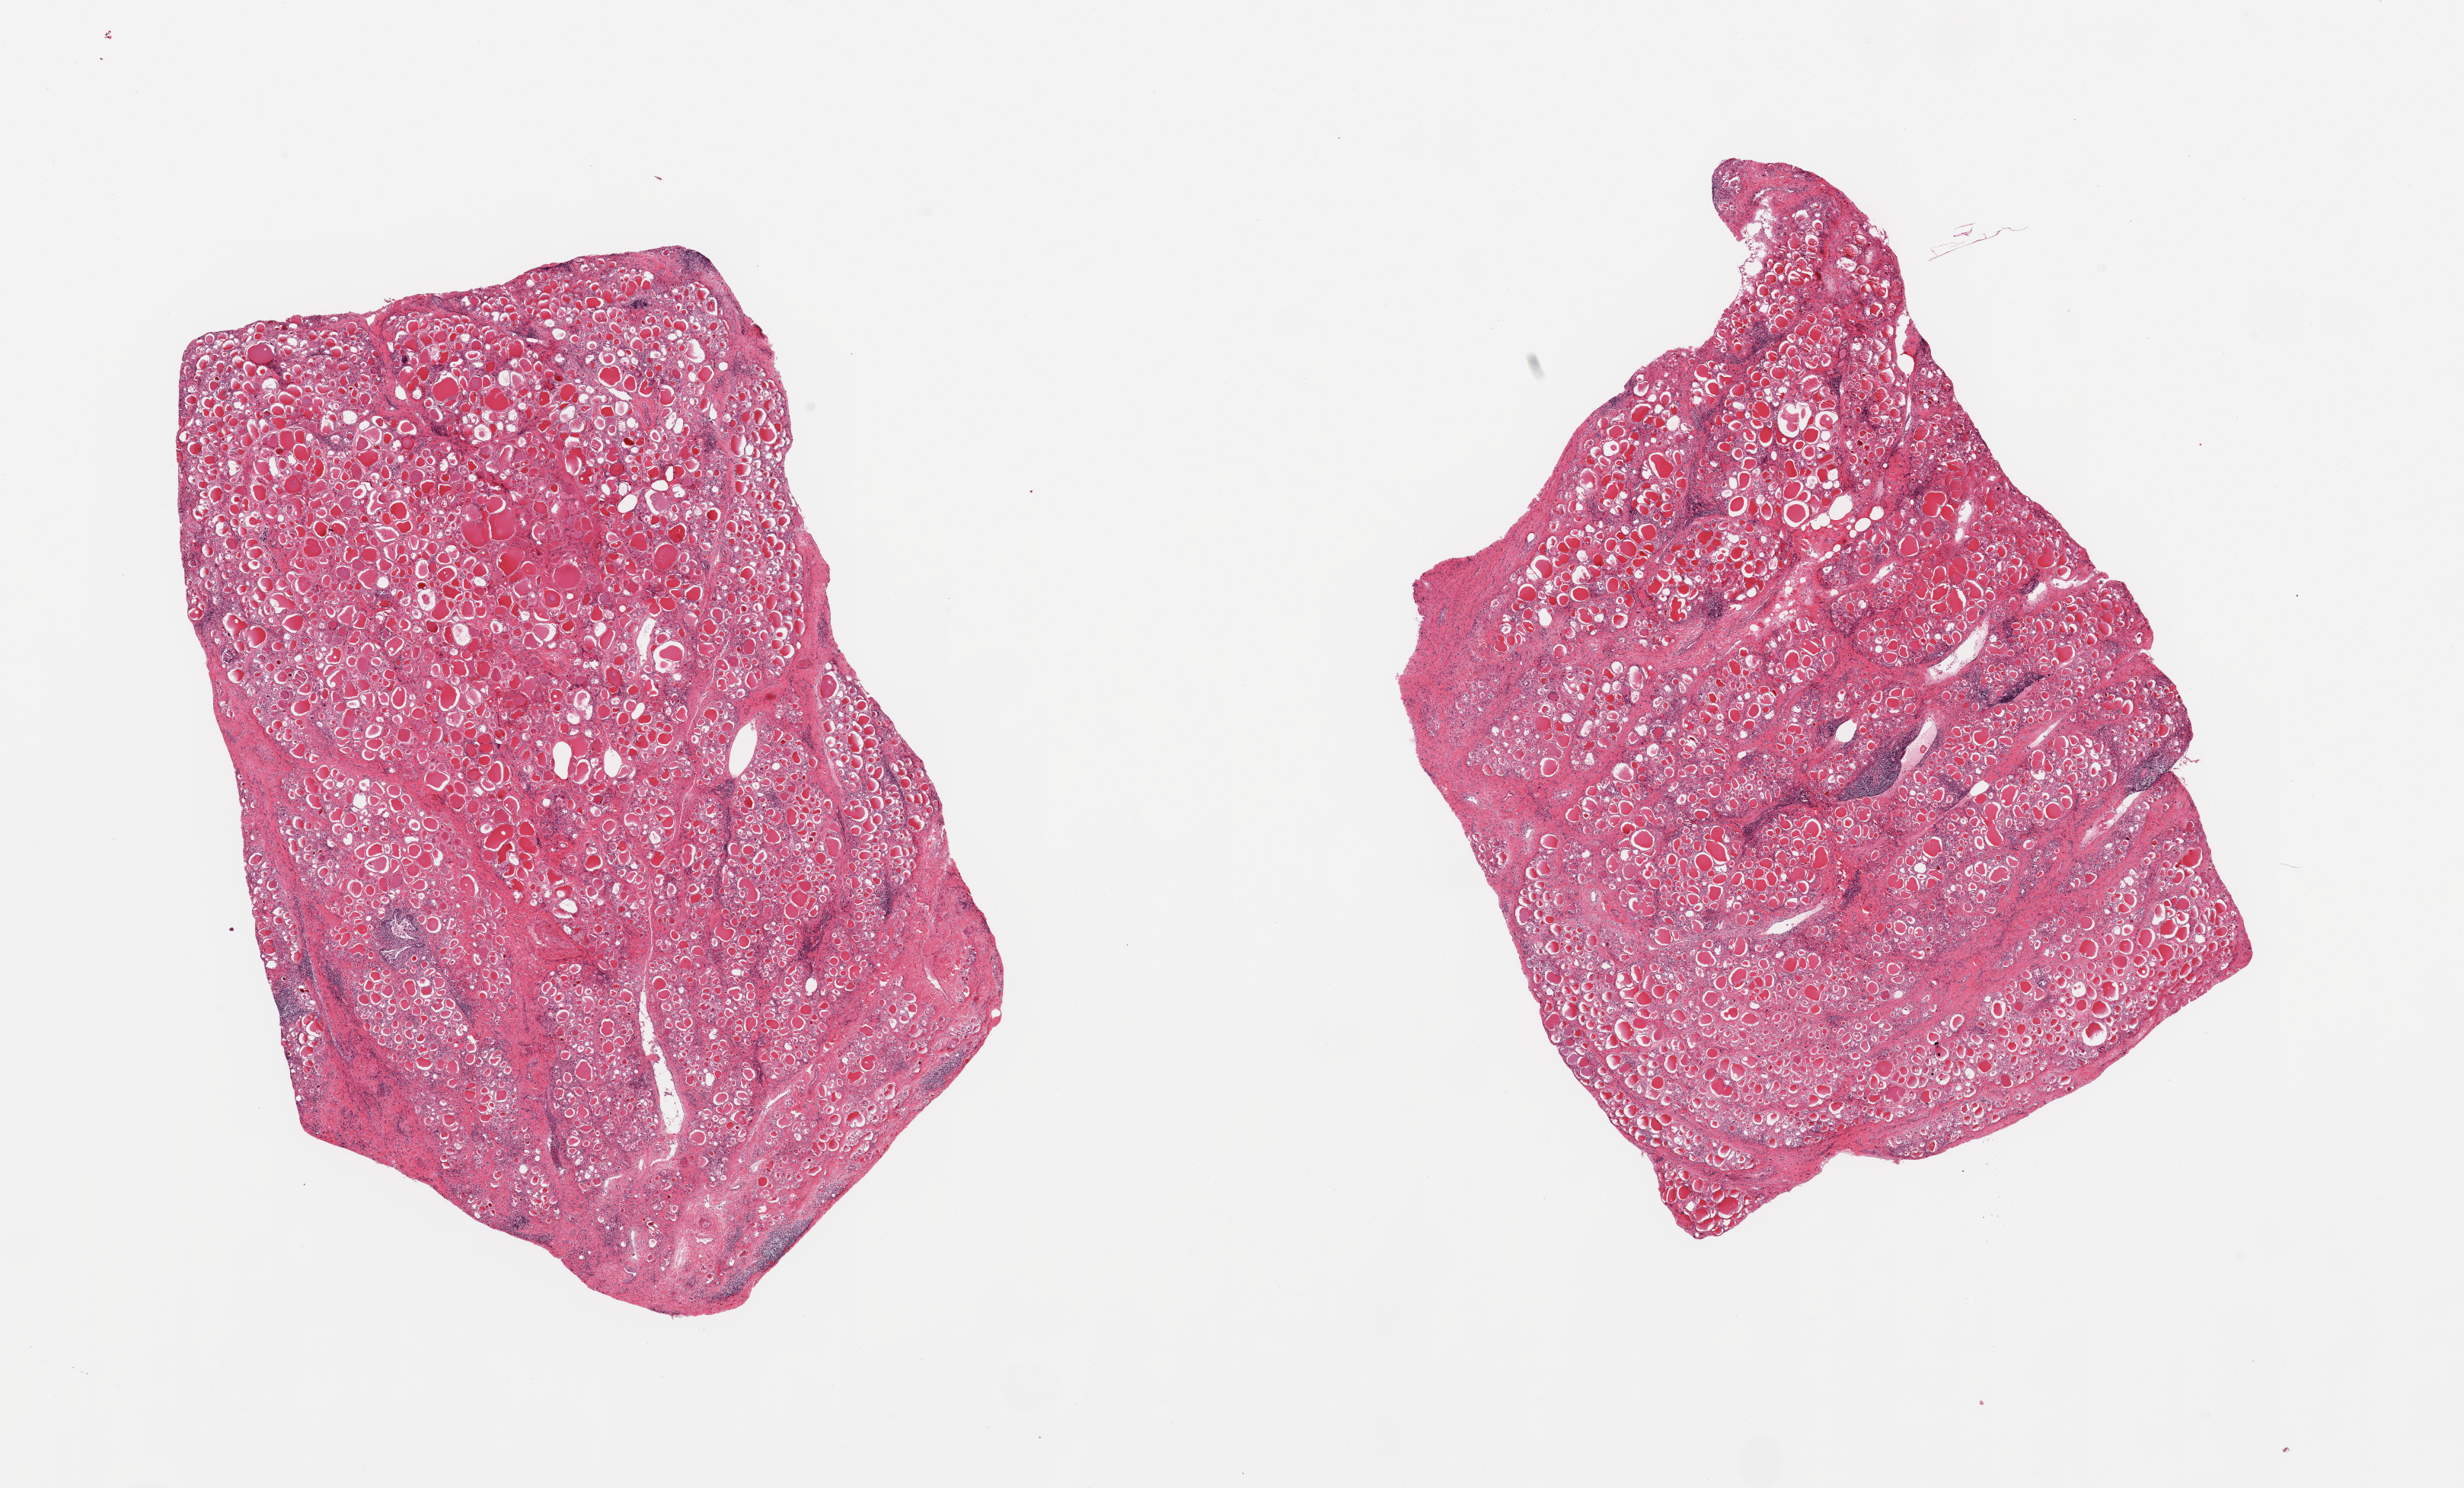
Whole-slide image, H&E stain, brightfield — low-resolution overview of the scanned area, about 25.6 x 15.5 mm (acquisition: 20x scan); PAXgene-fixed, paraffin-embedded tissue; target tissue: thyroid; donor tissue sample.
Review note (as recorded): 2 pieces; some fibrosis and nodularity with dispersed lymphocytic infiltrates.